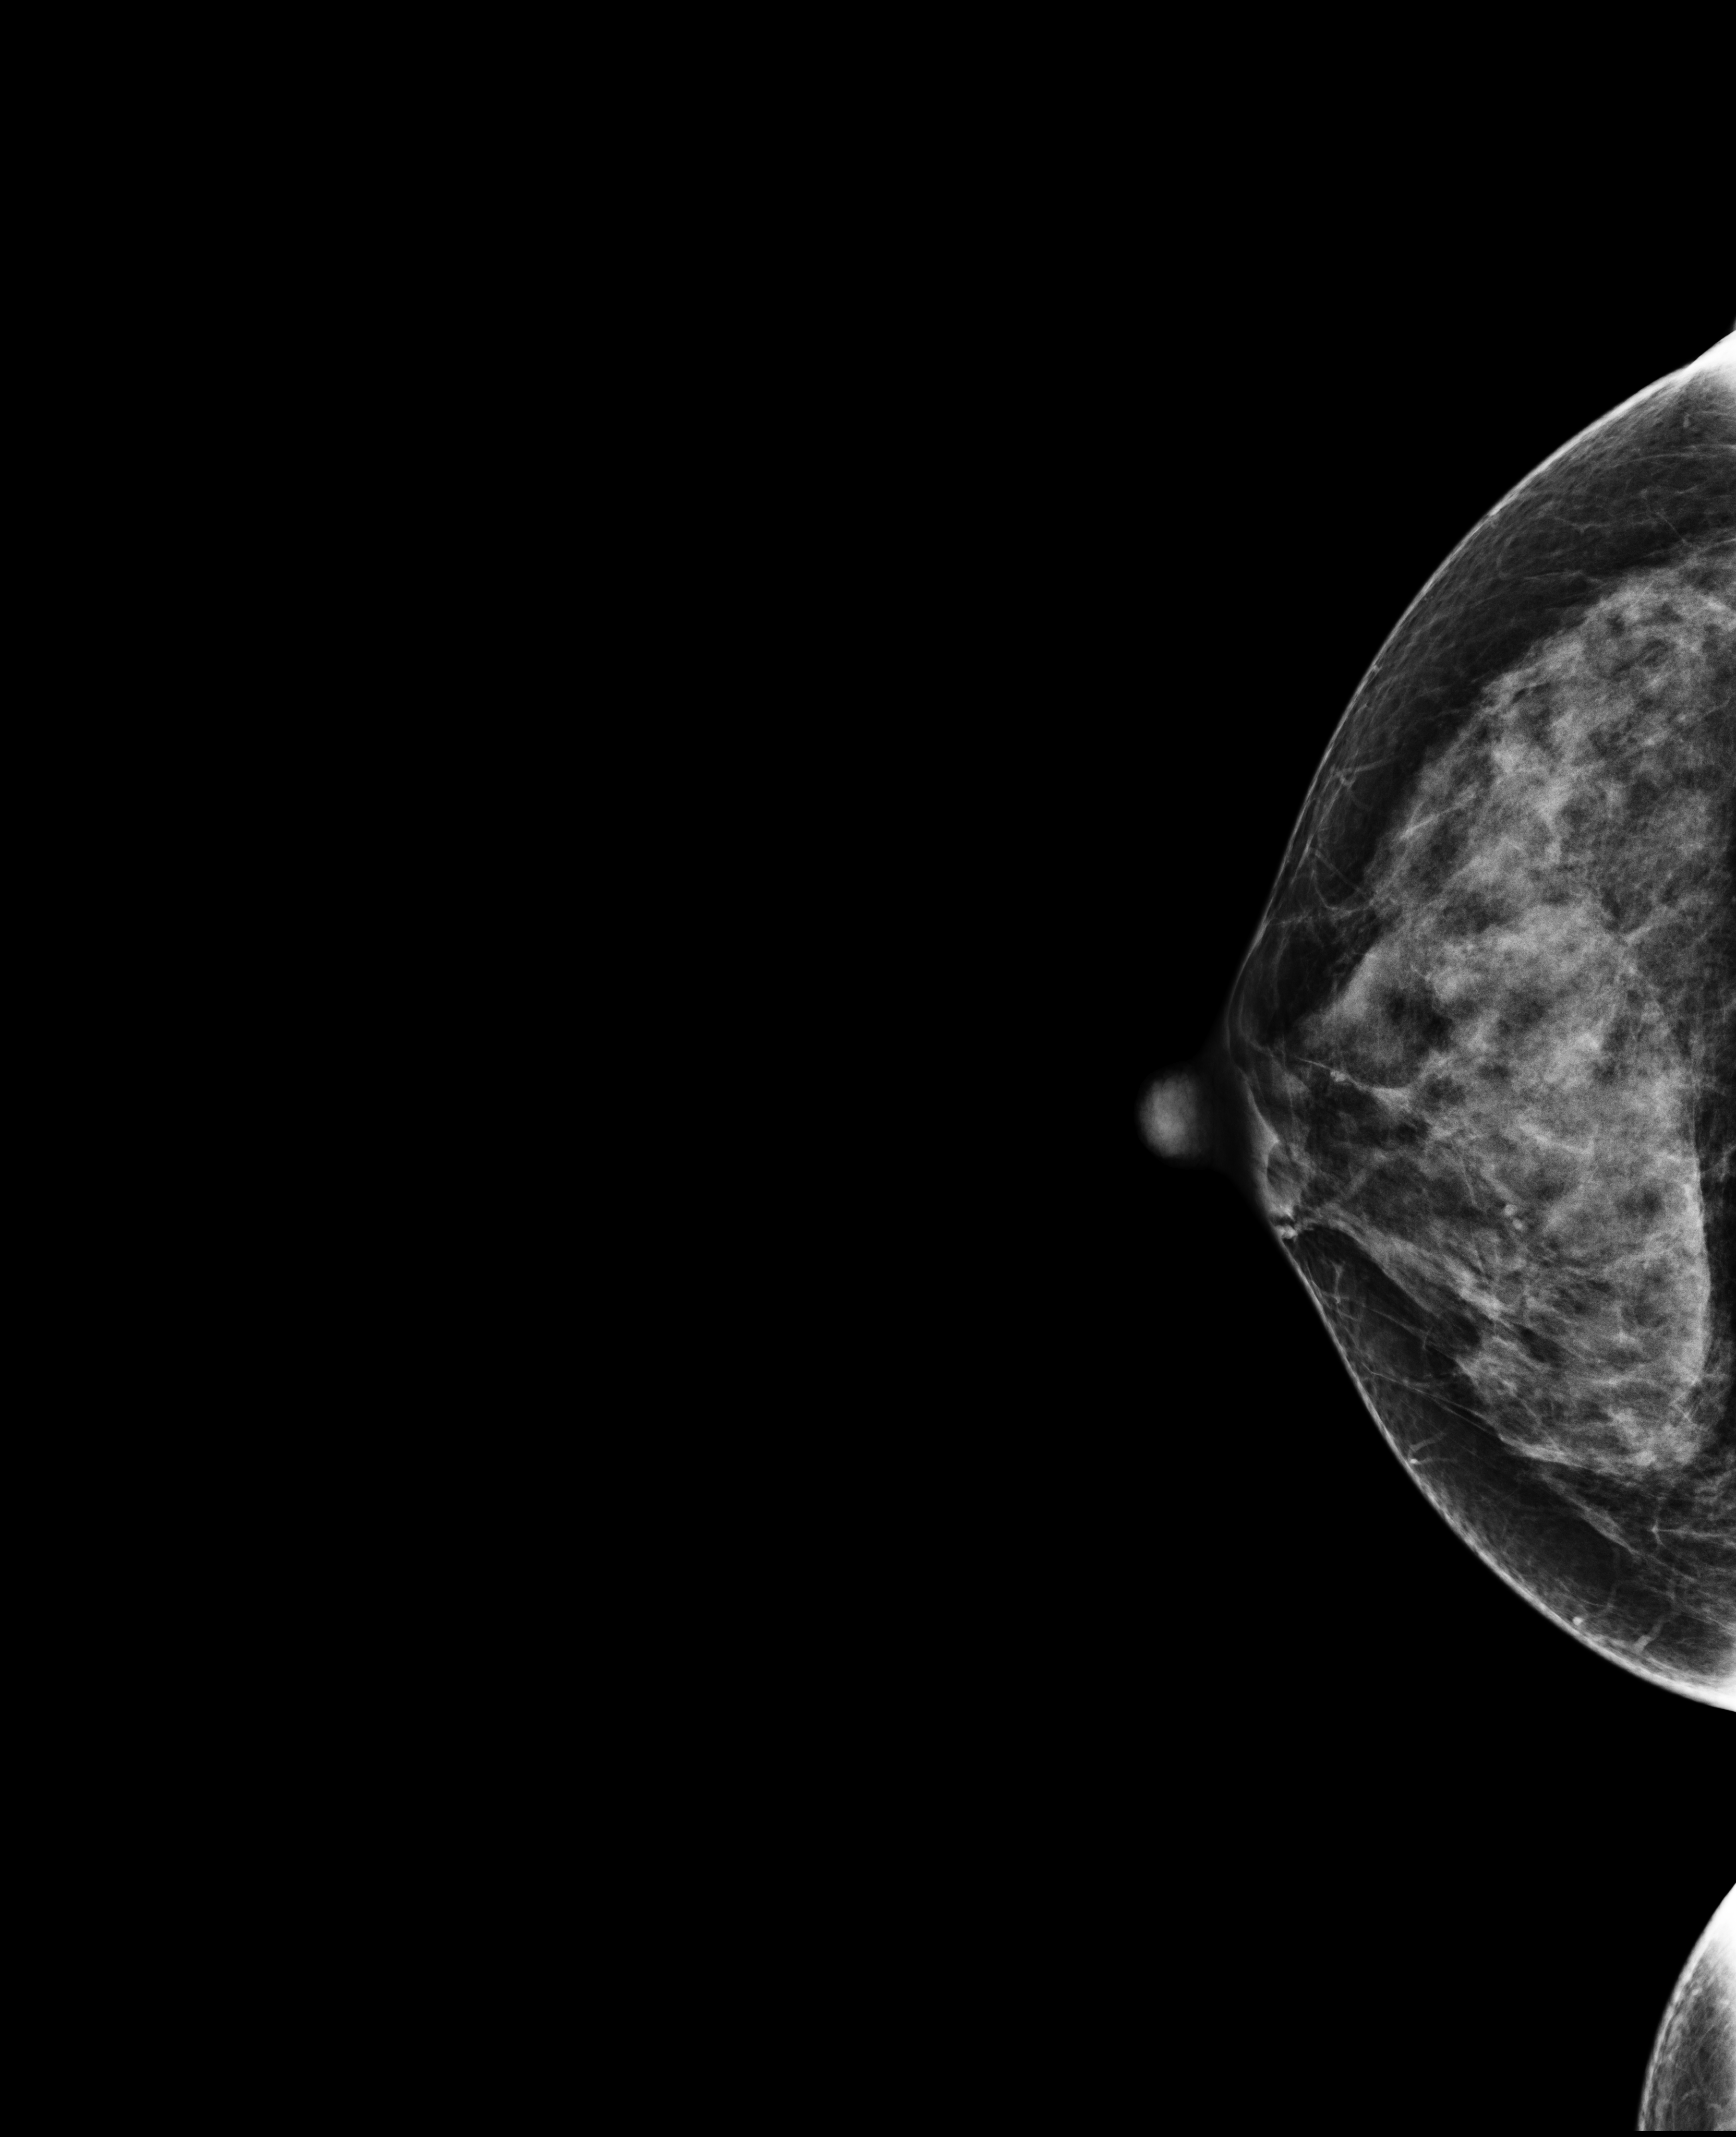
Annual screening mammography examination, compressed breast thickness 63 mm. Female patient, age 42 years.
Image type: full-field digital mammogram. Breast: right. Projection: CC view.